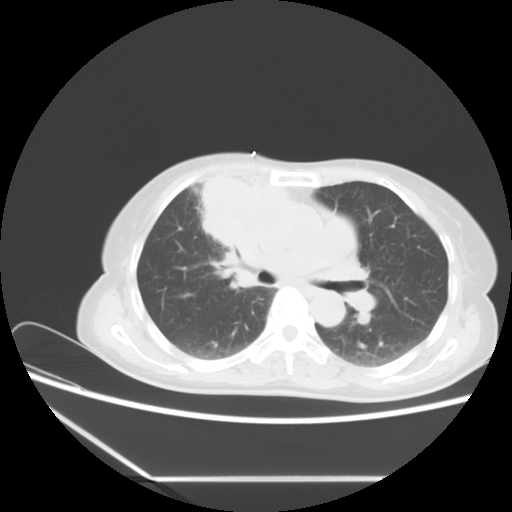
Chest CT, one axial slice; position 10 of 16 along the scan axis; reconstruction kernel STANDARD; lung window (W 1500 / L -600 HU); 5 mm slice thickness; 512 × 512 image matrix, field of view 350 × 350 mm. Female patient, age 63 years. From the clinical record (not read from this slice): clinical TNM (as recorded): T2b N1 M0.
Annotated regions visible in this slice (bounding box drawn by a radiologist):
- lung tumour (recorded histology: adenocarcinoma): bounding box [x1, y1, x2, y2] px = [194, 165, 289, 258]